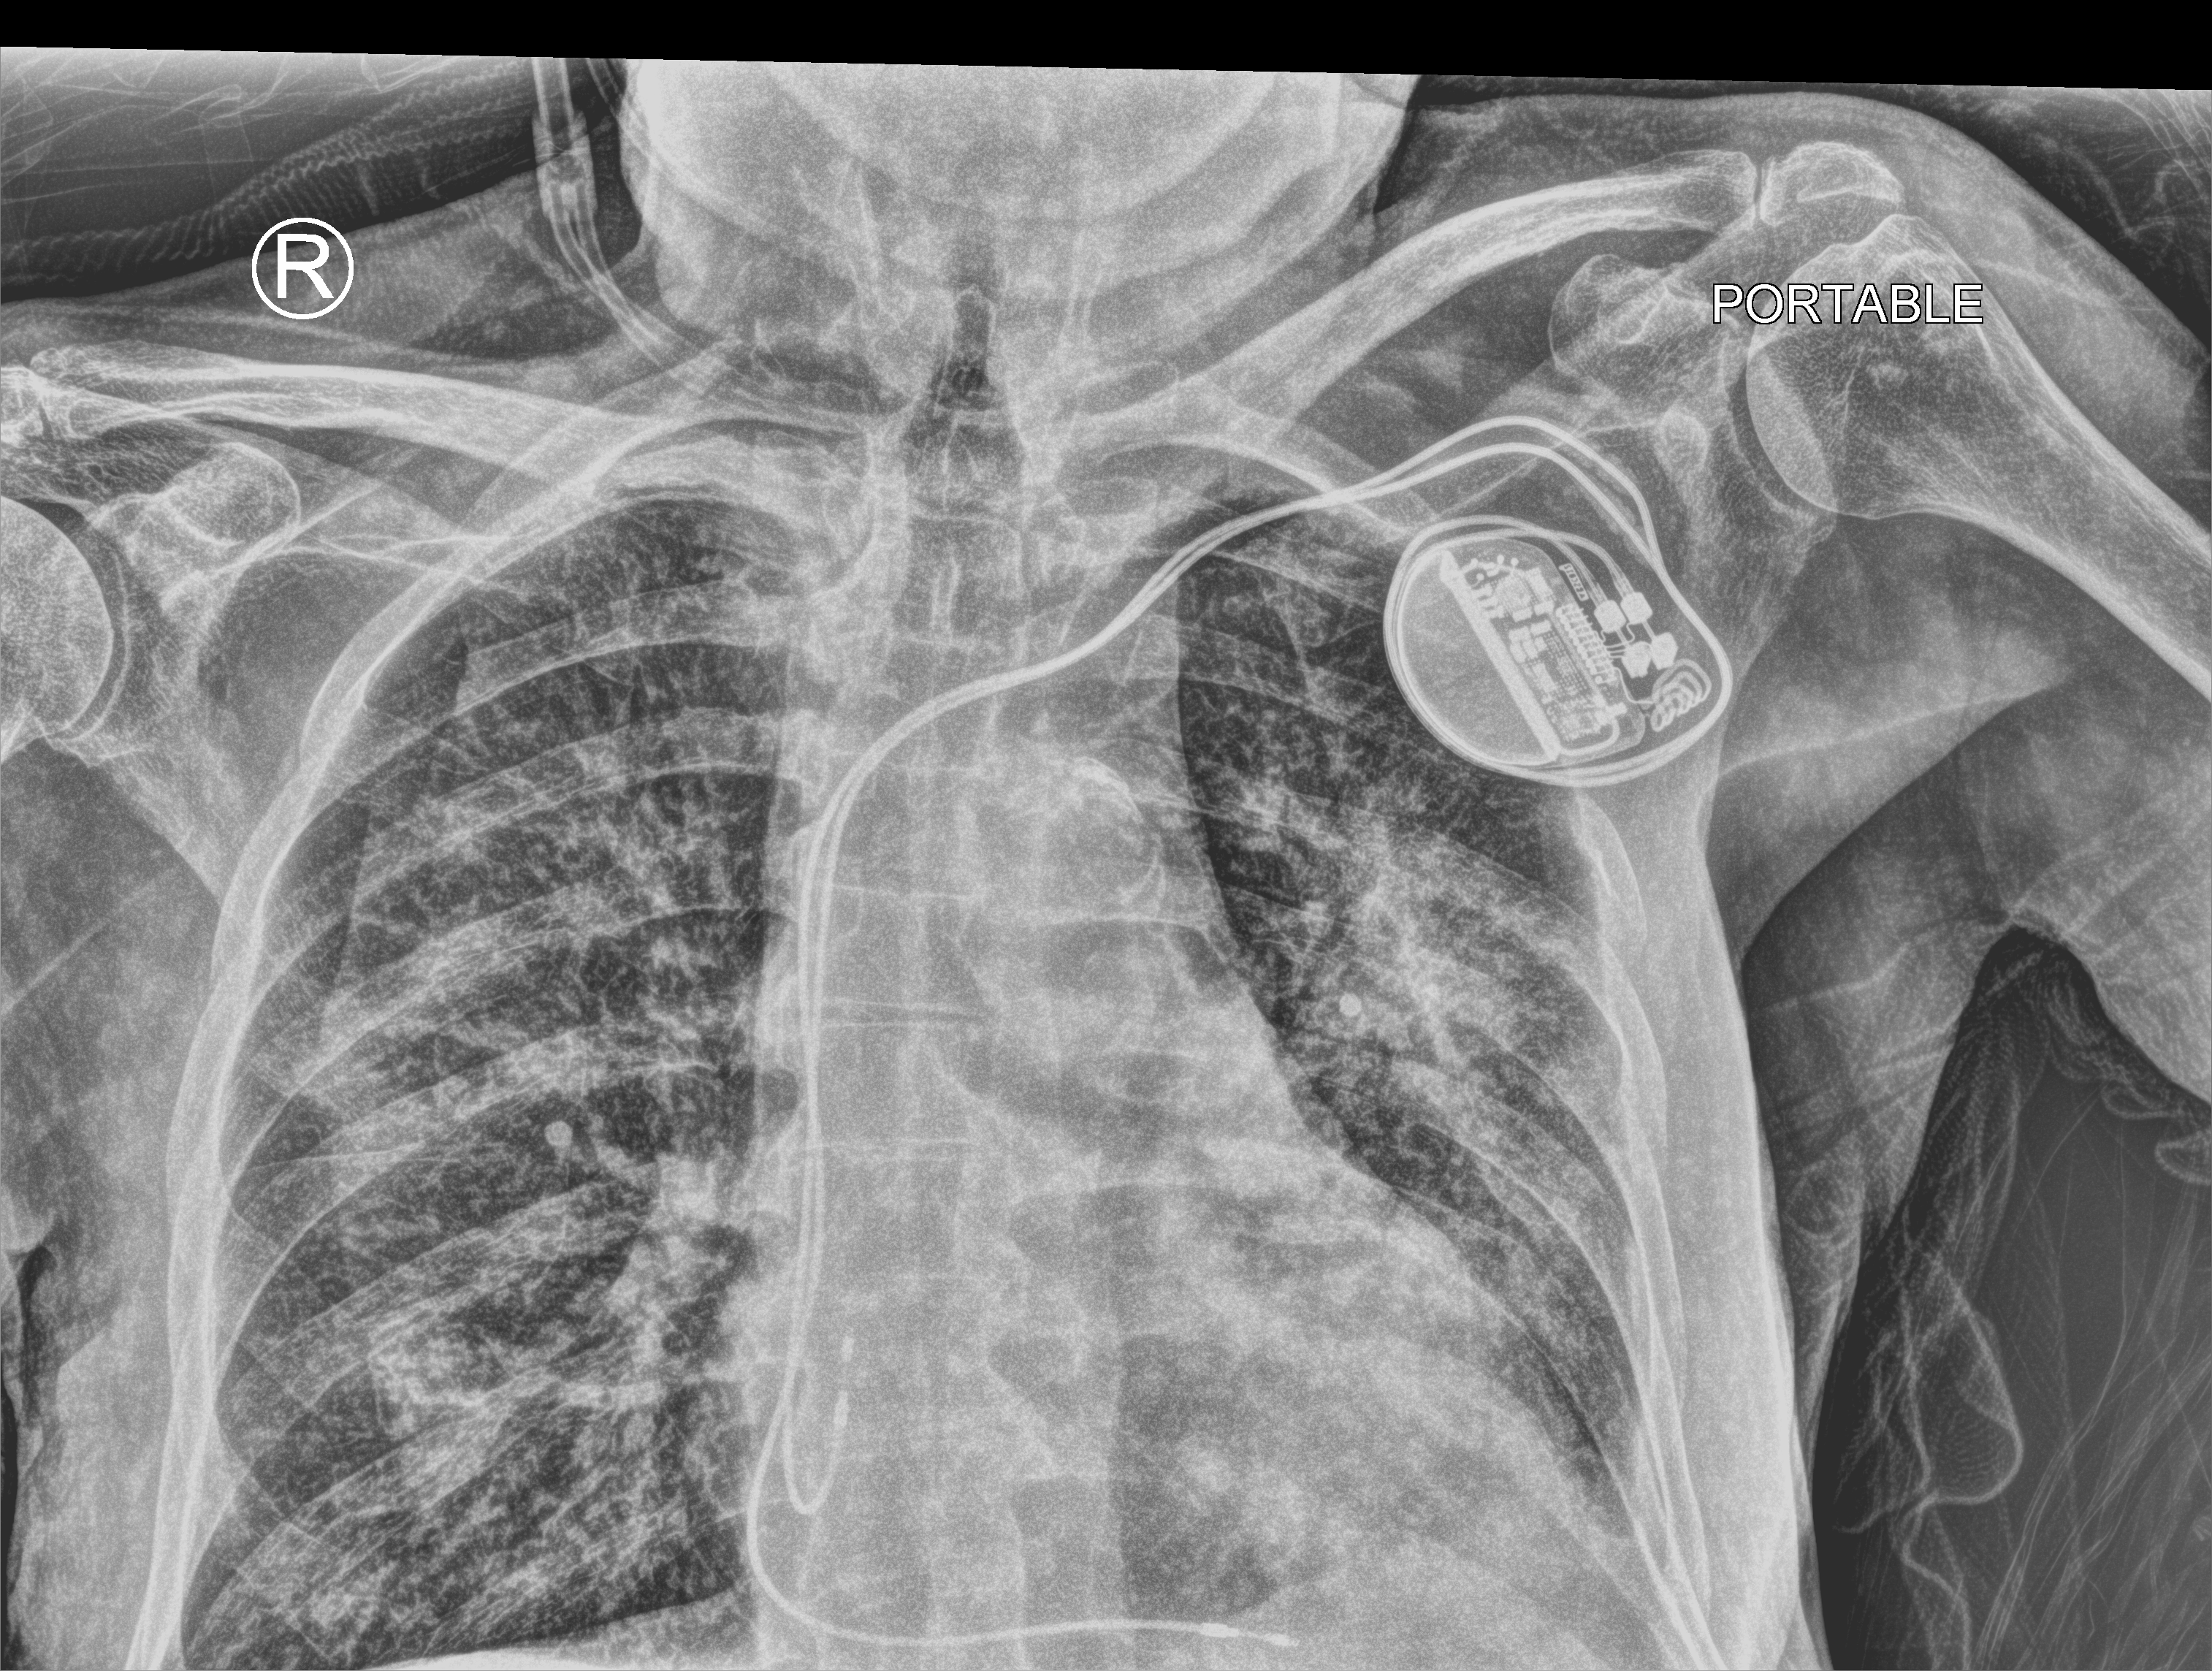
Portable chest radiograph; anteroposterior (AP) projection. Patient hospitalised with COVID-19; male, aged 75–90 years.
Hospital-stay facts (about this admission, not read from this image; timing relative to this image not recorded): admitted to intensive care during this hospital stay: no.